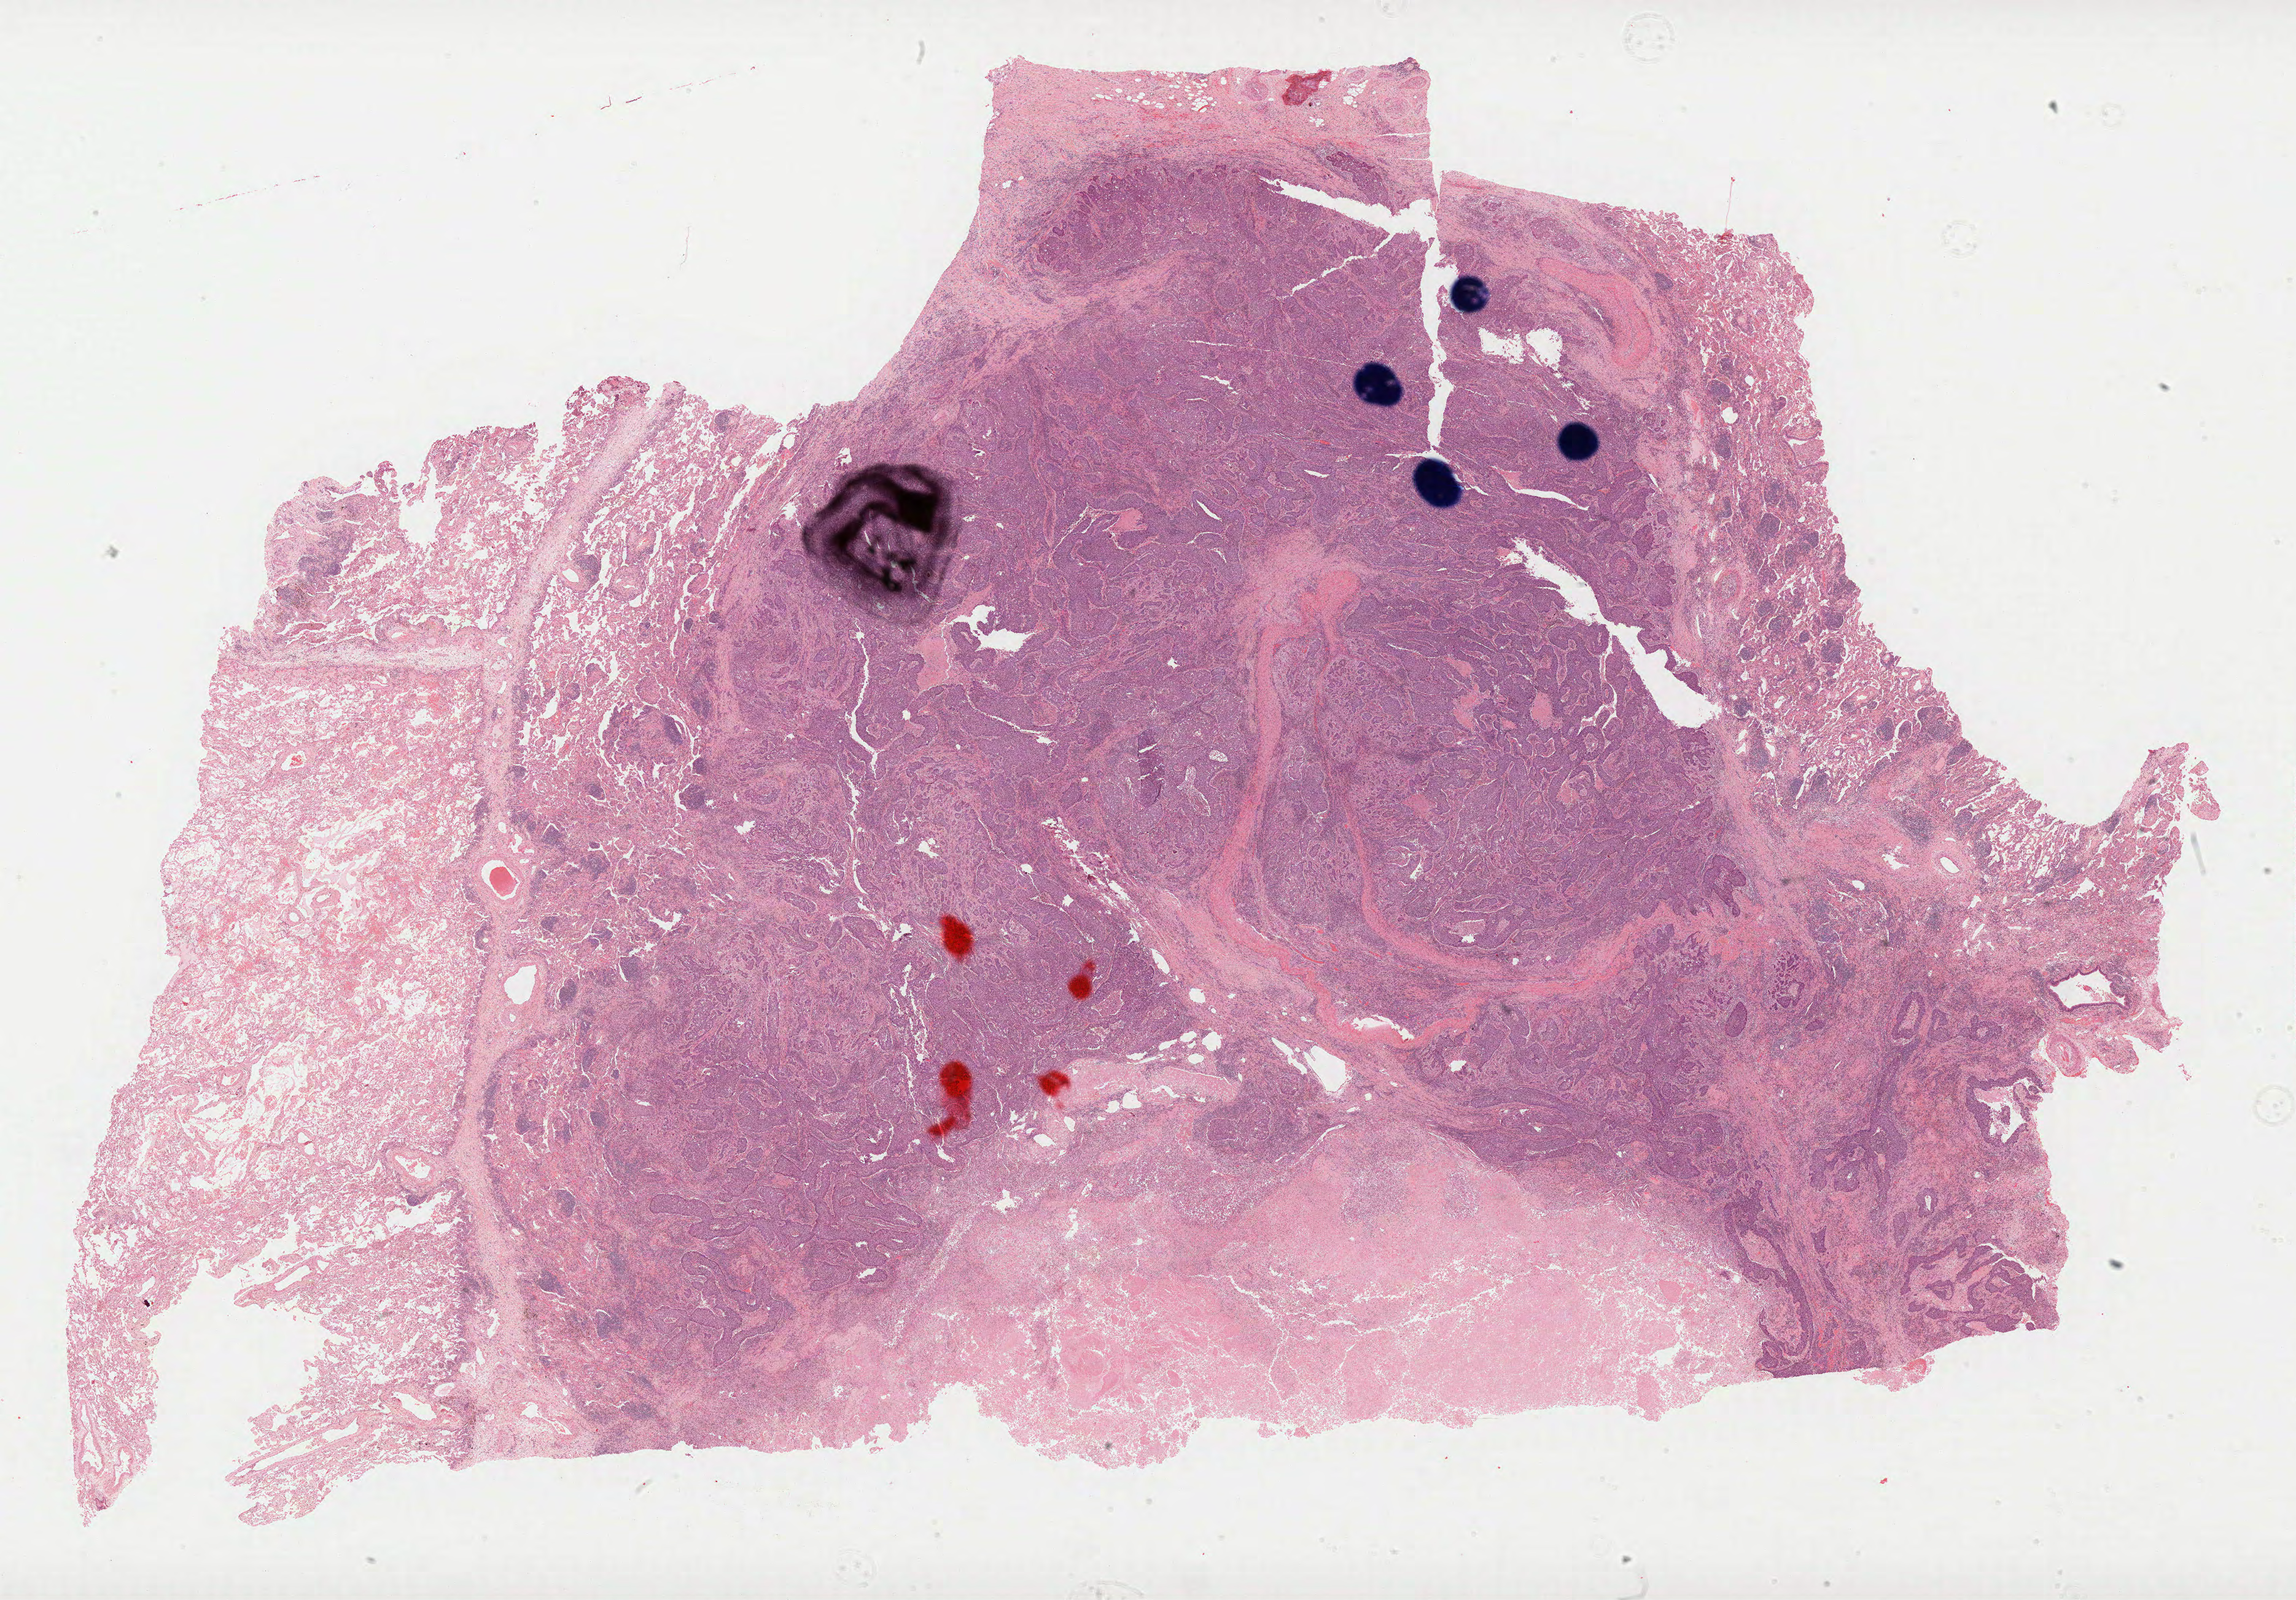
Digitized H&E-stained tissue section (whole slide), shown as a low-resolution overview of the whole scanned area (about 30.2 x 21.0 mm, slide scanned at 40x), formalin-fixed paraffin-embedded (FFPE) diagnostic section, lung, primary tumour sample. Female, age 63 years at initial diagnosis.
Diagnosis: Squamous cell carcinoma, NOS. Laterality: right. AJCC pathologic stage: IIIA.